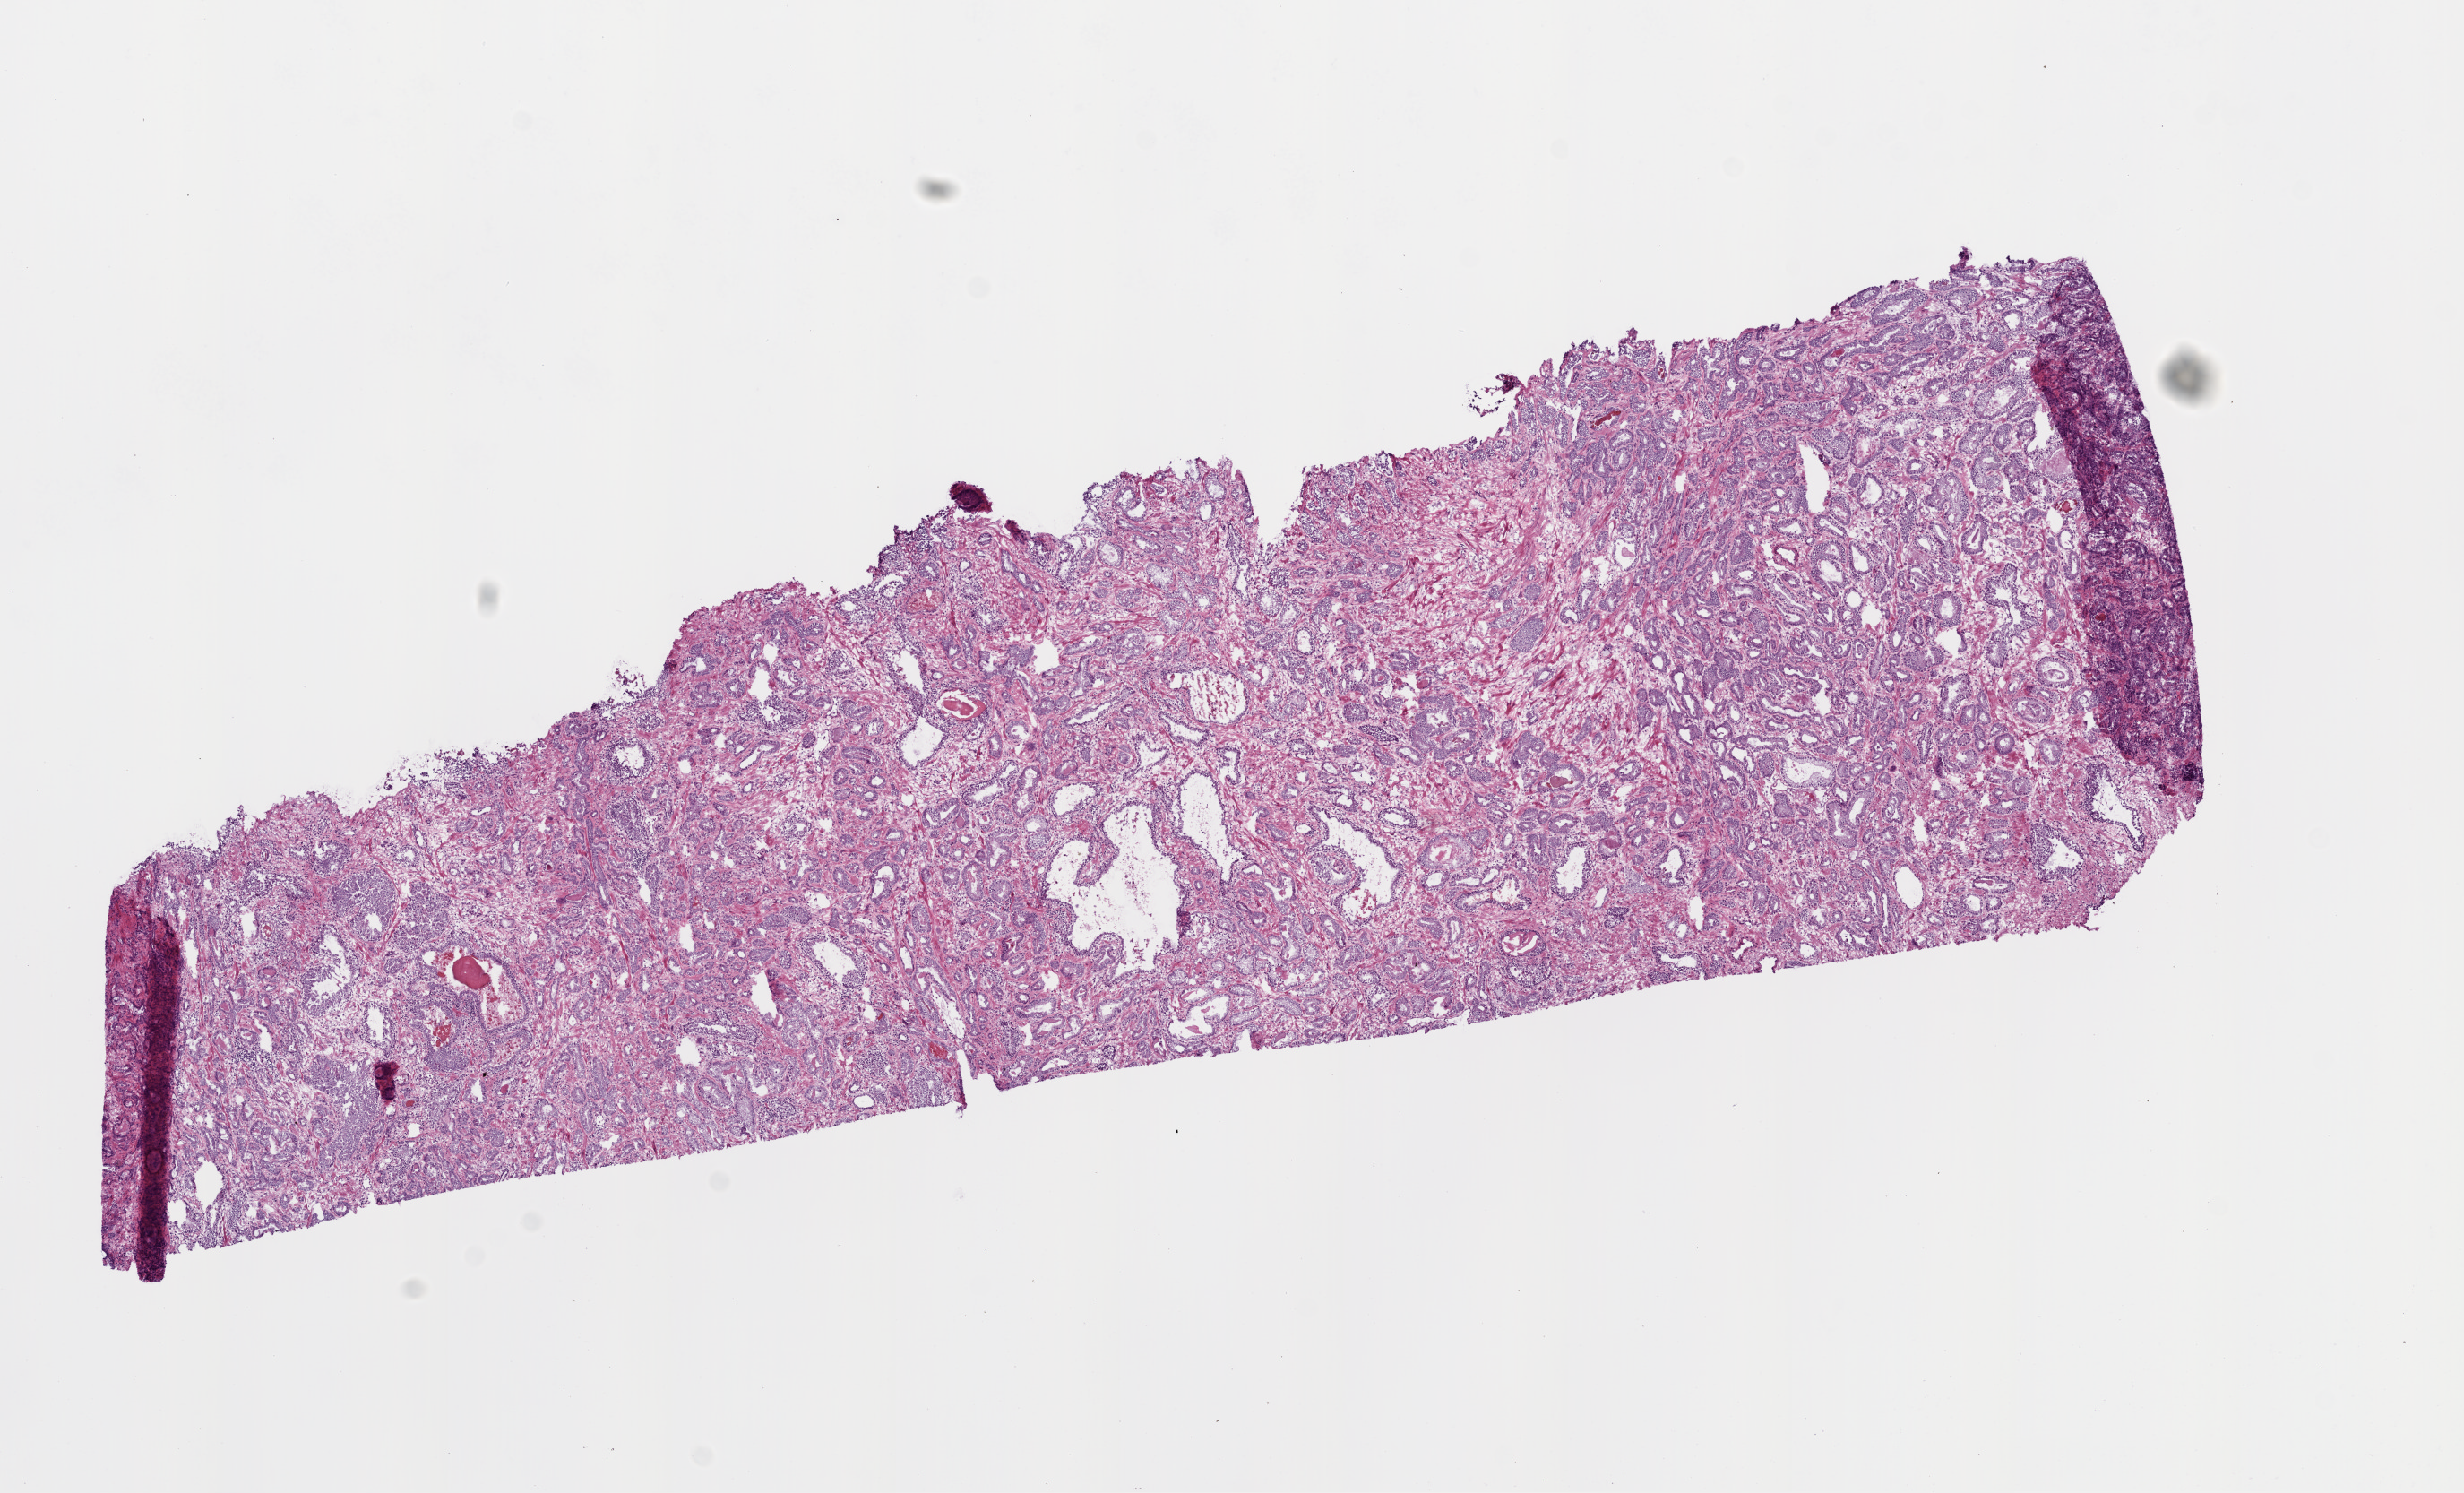
H&E-stained whole-slide image, shown as a low-resolution overview of the whole scanned area (about 11.0 x 6.7 mm, acquisition: 20x scan). Frozen section from the top of the tissue portion. Prostate, primary tumour sample. Male patient; age at initial diagnosis 72 years. Gleason score: 6 (3+3). Pathologist review of this section (percent, as recorded): tumour cells 70%, tumour nuclei 70%, normal cells 15%, stromal cells 15%, necrosis 0%. Inflammatory infiltration, as recorded: lymphocyte infiltration 2%, monocyte infiltration 0%, neutrophil infiltration 0%.
- histologic diagnosis: Acinar cell carcinoma (prostate gland)